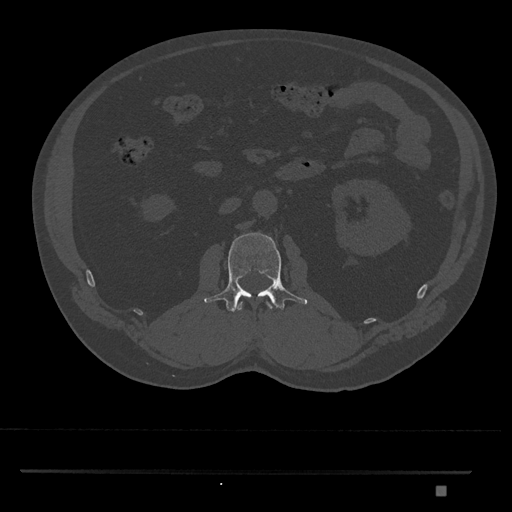
CT including the spine, one axial slice. Position 761 of 1134 along the scan axis. Reconstruction kernel Br40s/3. Bone window (W 1800 / L 400 HU). 0.5 mm slice thickness. 512 × 512 image matrix. Male patient, age 65 years. Case-level facts recorded for this patient, not image findings: primary cancer: prostate.
Outlined on this slice (semi-automatic segmentation, software-assisted and operator-edited):
- L1 vertebra: box from (x=236, y=302) to (x=273, y=311) px
- L2 vertebra: (x=204, y=233)–(x=308, y=312)